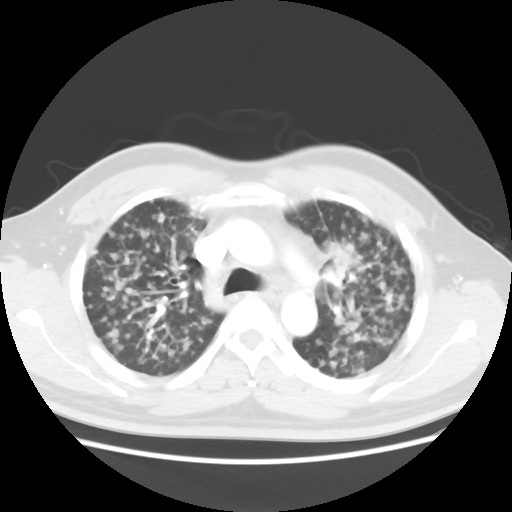
Chest CT, one axial slice; position 27 of 40 along the scan axis; 120 kVp; lung window (W 1500 / L -600 HU); 5 mm slice thickness; 512 × 512 image matrix, field of view 366 × 366 mm. Male patient, age 41 years. From the clinical record (not read from this slice): clinical TNM (as recorded): T1c N3 M1b.
Annotated regions visible in this slice (rectangle marked by the reading radiologist):
- lung tumour (recorded histology: adenocarcinoma): bounding box <327,240,354,285> (left, top, right, bottom; pixels)